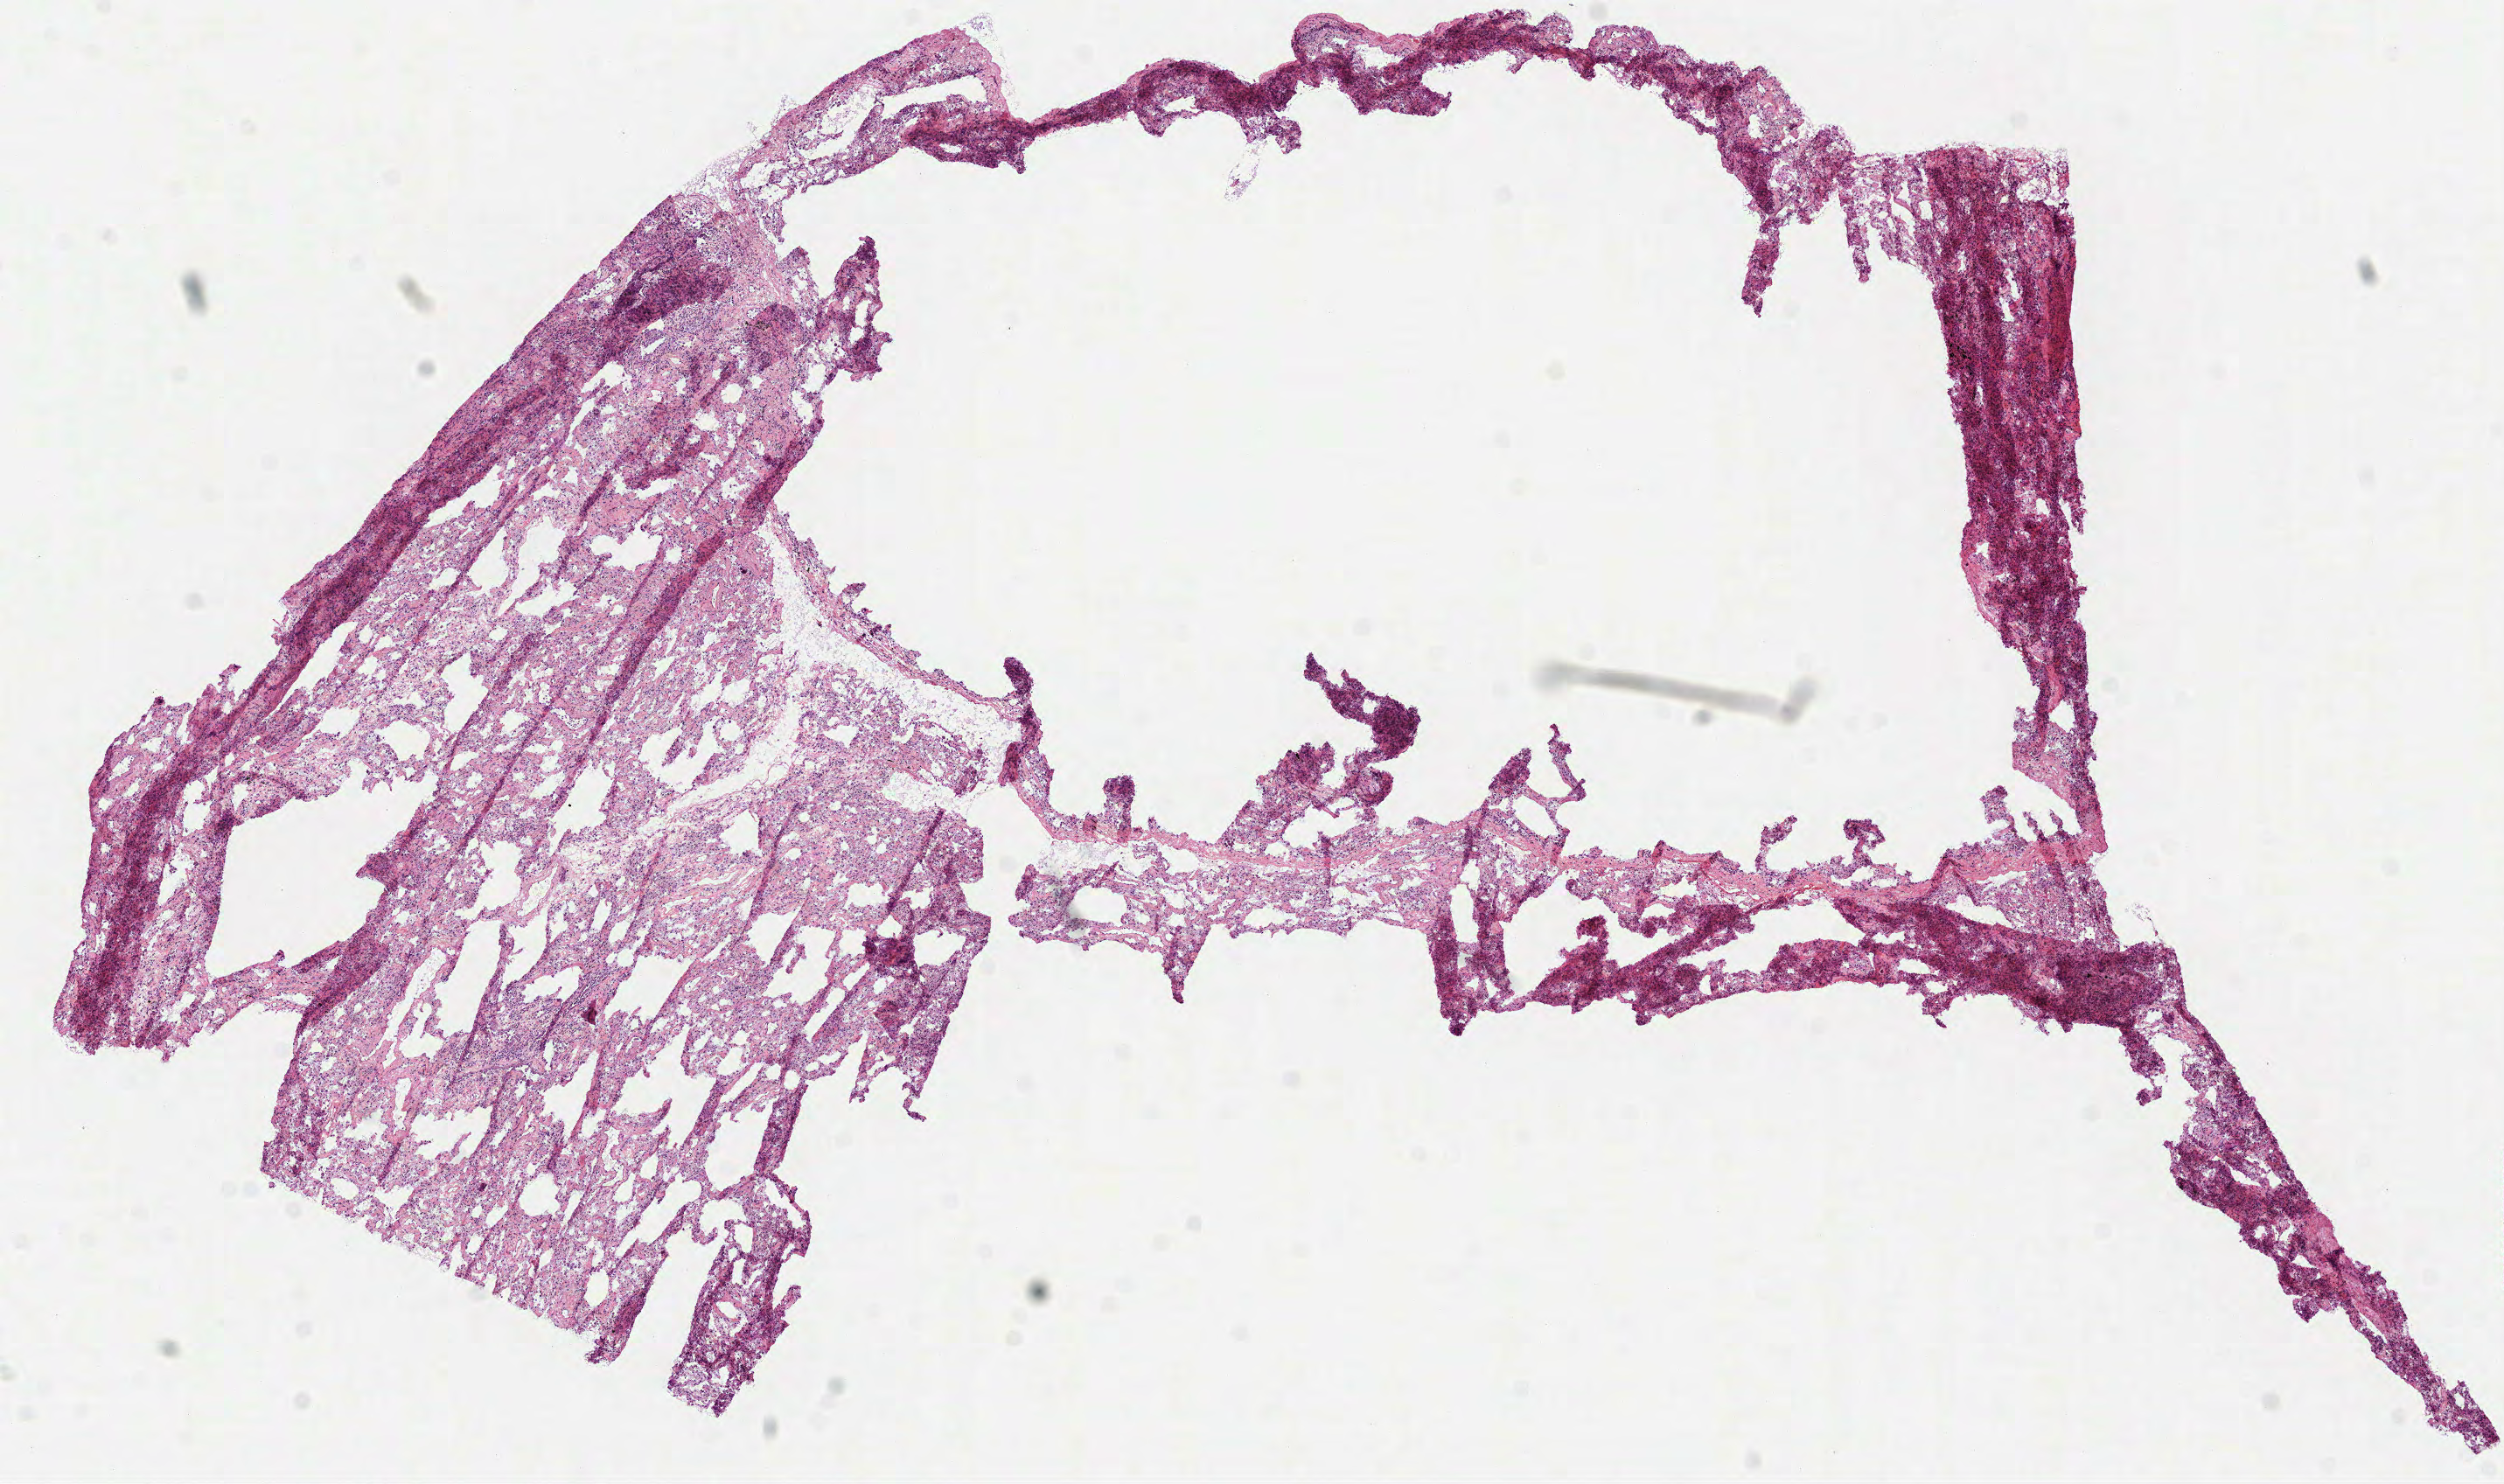
H&E-stained whole-slide image — shown as a low-resolution overview of the whole scanned area (about 11.5 x 6.8 mm, slide scanned at 40x). Frozen section from the top of the tissue portion. Solid tissue normal (non-tumour tissue) sample from the lung. Patient: female, age at initial diagnosis 69 years.
This section: solid tissue normal (non-tumour) sample from the same patient. Patient diagnosis: Squamous cell carcinoma, NOS (lower lobe, lung).